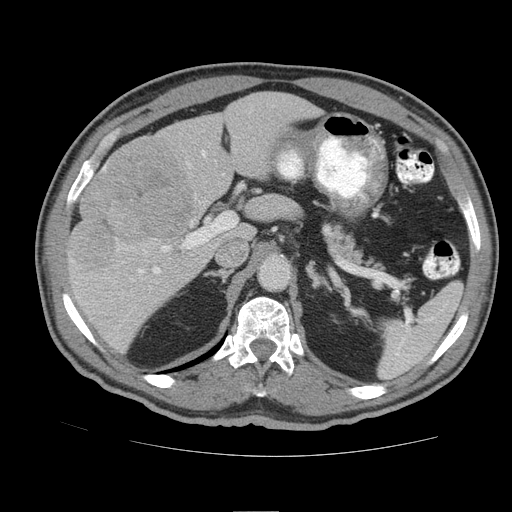
Contrast-enhanced abdominal CT (liver protocol), one axial slice. Slice 55 of 105 in the series (ordered by position). Reconstruction kernel STANDARD. 140 kVp. Soft-tissue window (W 400 / L 40 HU). 2.5 mm slice thickness. 512 × 512 image matrix, field of view 380 × 380 mm. Case-level facts recorded for this patient, not image findings: diagnosis: hepatocellular carcinoma (patient treated with transarterial chemoembolisation; whether this scan precedes or follows treatment is not stated here); TNM stage (as recorded): Stage-IIIB; Child-Pugh class: A.
Annotated regions visible in this slice (semi-automatic segmentation, software-assisted and operator-edited):
- liver parenchyma outside the tumour (the mass and vessels are separate outlines, so this box may not span the whole liver): bounding box (x1, y1, x2, y2) in pixels: (66, 92, 322, 352)
- mass: (71, 140, 197, 269)
- liver vessels: (103, 151, 217, 274)